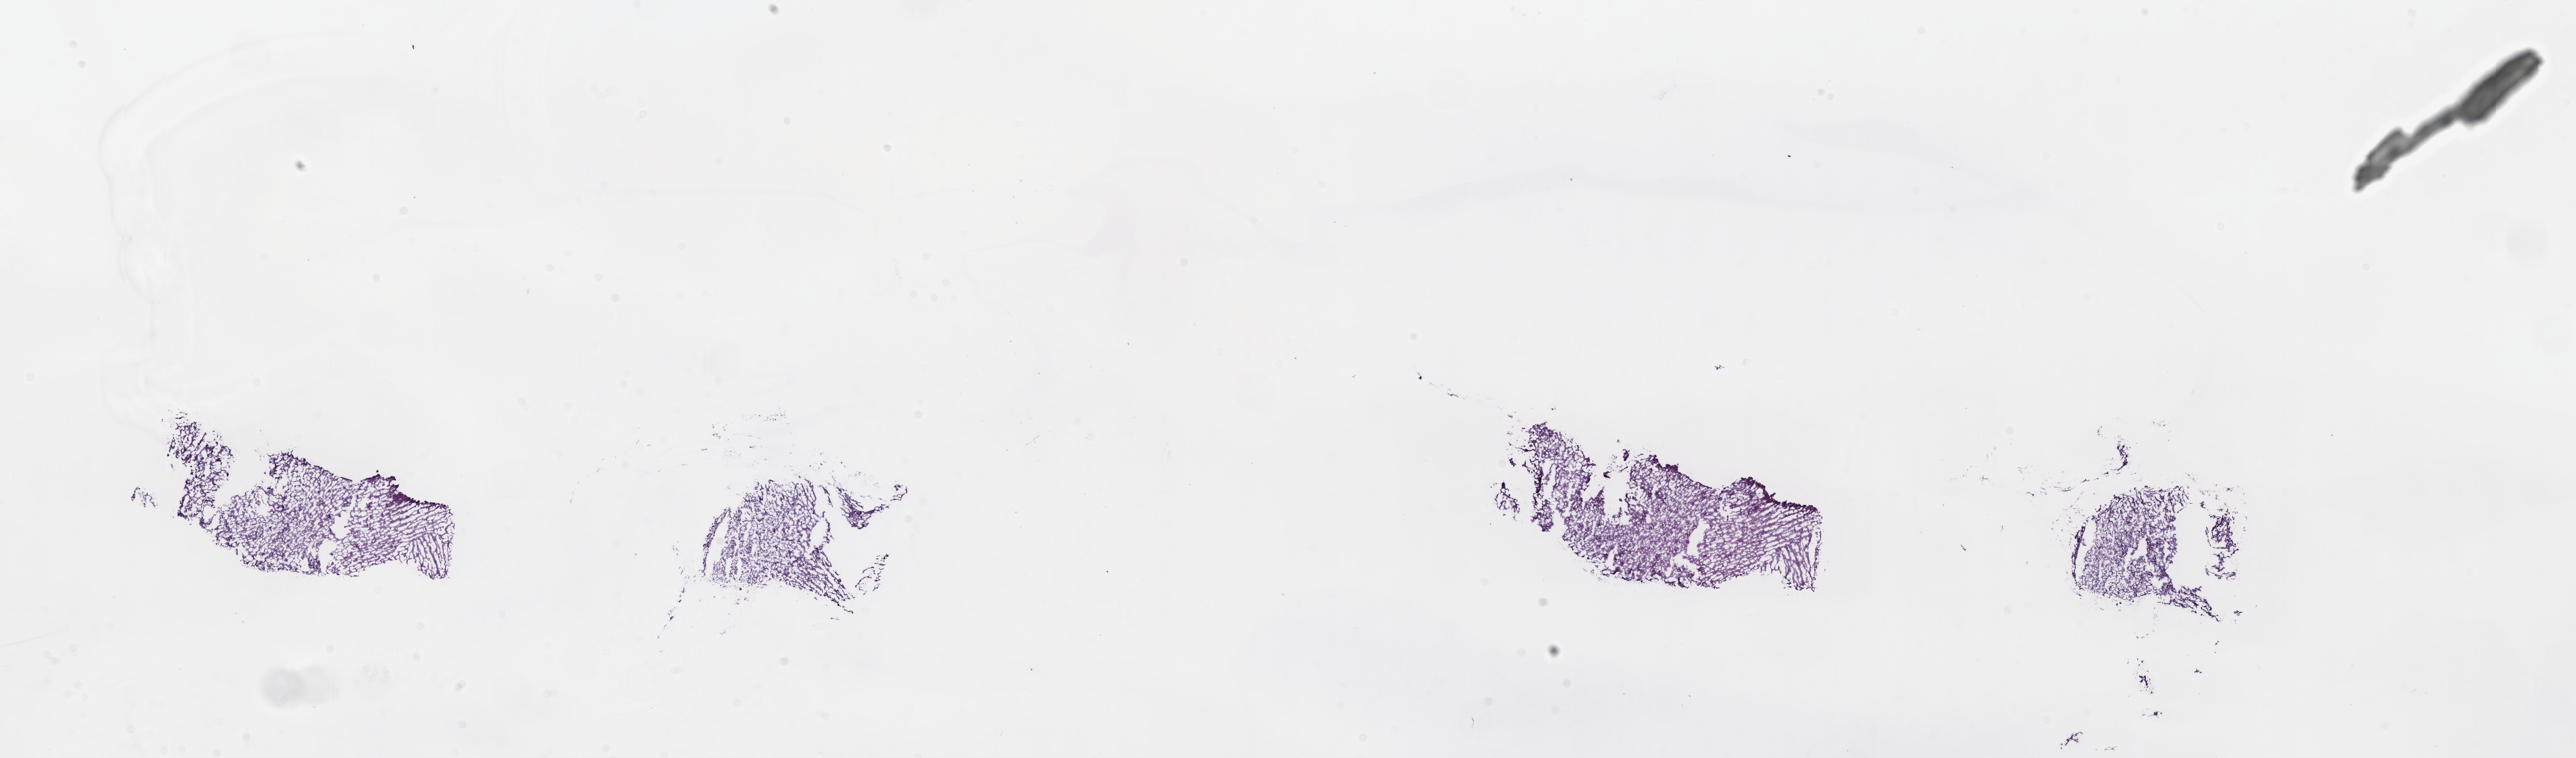
H&E whole-slide image — whole scanned area (about 31.2 x 9.2 mm, from a 40x scan) shown as a low-resolution overview. Frozen section from the top of the tissue portion. Brain, primary tumour sample. Patient: female, age at initial diagnosis 34 years.
Histologic diagnosis: Astrocytoma, NOS (cerebrum).